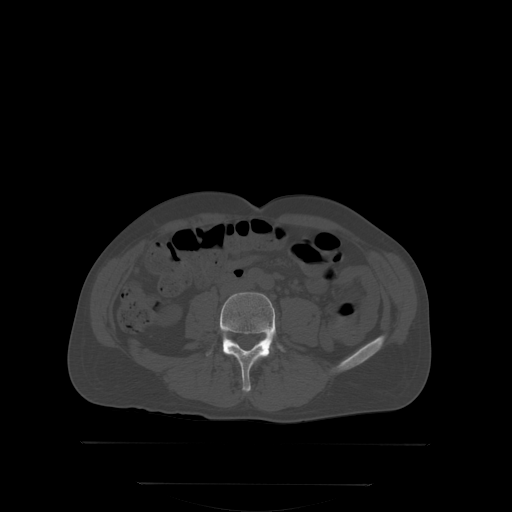
CT including the spine, one axial slice. Bone window (W 1800 / L 400 HU). 512 × 512 image matrix. Male patient, age 58 years. From the clinical record (not read from this slice): primary cancer: prostate; vertebrae with lytic lesions (as recorded): L1.
Annotated regions visible in this slice (semi-automatically segmented with operator editing):
- L4 vertebra: bounding box [x1, y1, x2, y2] px = [206, 292, 285, 392]